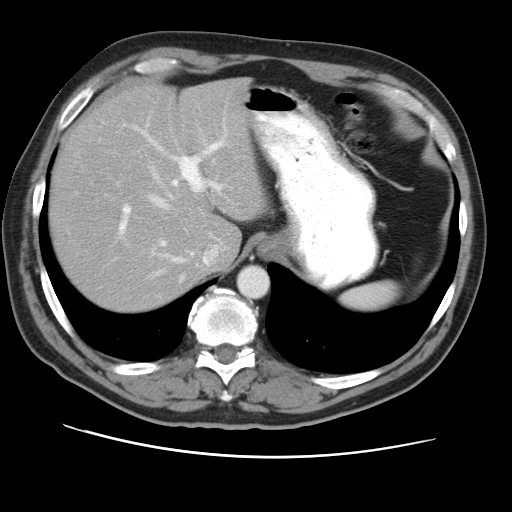
Contrast-enhanced abdominal CT, one axial slice. Position 37 of 49 along the scan axis. Reconstruction kernel STANDARD. 120 kVp. Intravenous contrast given. Soft-tissue window (W 400 / L 40 HU). 5 mm slice thickness. 512 × 512 image matrix, field of view 374 × 374 mm. Male patient, age 59 years. From the clinical record (not read from this slice): diagnosis: colorectal cancer liver metastases, imaged before liver resection; multiple liver metastases: yes; largest metastasis: 6.3 cm; disease in both lobes: yes.
Annotated regions visible in this slice (outlined manually by an expert reader):
- hepatic veins: bounding box [x1, y1, x2, y2] px = [151, 129, 226, 274]
- liver: [51, 80, 265, 311]
- planned liver remnant (the part of the liver to remain after resection): [51, 80, 265, 311]
- portal vein (with intrahepatic branches): [119, 124, 223, 246]